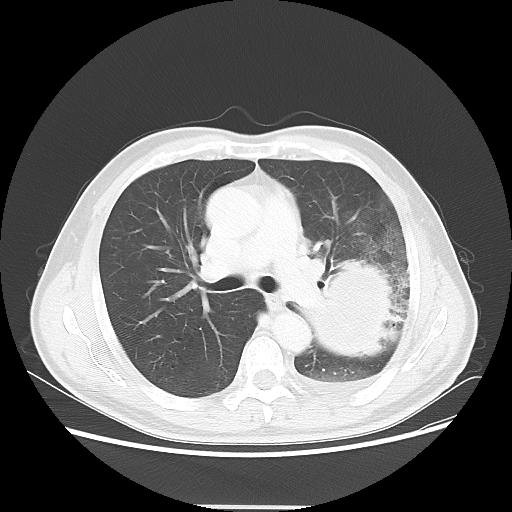
Chest CT, one axial slice. Slice 33 of 53 in the series (ordered by position). Reconstruction kernel LUNG. Lung window (W 1500 / L -600 HU). 5 mm slice thickness. 512 × 512 image matrix, field of view 391 × 391 mm. Male patient, age 60 years. Case-level facts recorded for this patient, not image findings: clinical TNM (as recorded): T4 N1 M1a.
Structures marked on this image (rectangle marked by the reading radiologist):
- lung tumour (recorded histology: large cell carcinoma): bounding box (x1, y1, x2, y2) in pixels: (301, 248, 403, 367)